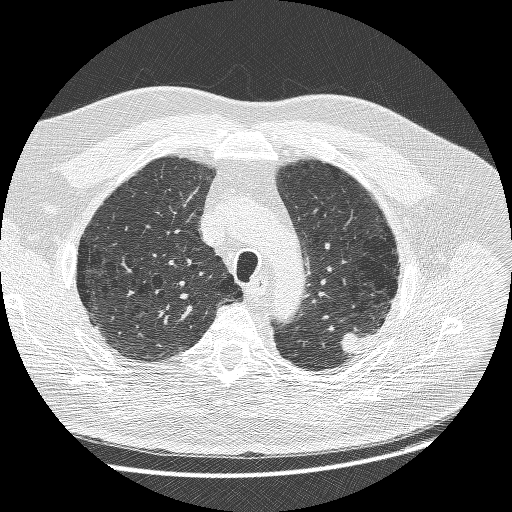
Chest CT (low-dose screening protocol), one axial image, baseline annual screen, lung window (W 1500 / L -600 HU), 1.25 mm slice thickness, slice 204 of 258 in the series, 512 × 512 image matrix, field of view 370 × 370 mm. Male participant, aged 68 years at enrolment. Former smoker at enrolment.
Expert-annotated lung lesion, bounding box <331,321,389,365> (left, top, right, bottom; pixels). Screening reader's record for this exam (one nodule recorded; not confirmed to be the boxed lesion): non-calcified nodule or mass ≥4 mm, left upper lobe, 15 × 14 mm, smooth margins, soft tissue attenuation. Lung cancer was diagnosed 19 days after this screen: adenosquamous carcinoma, left upper lobe, poorly differentiated (G3), stage IIIB (AJCC 6th edition), 32 mm at pathology.